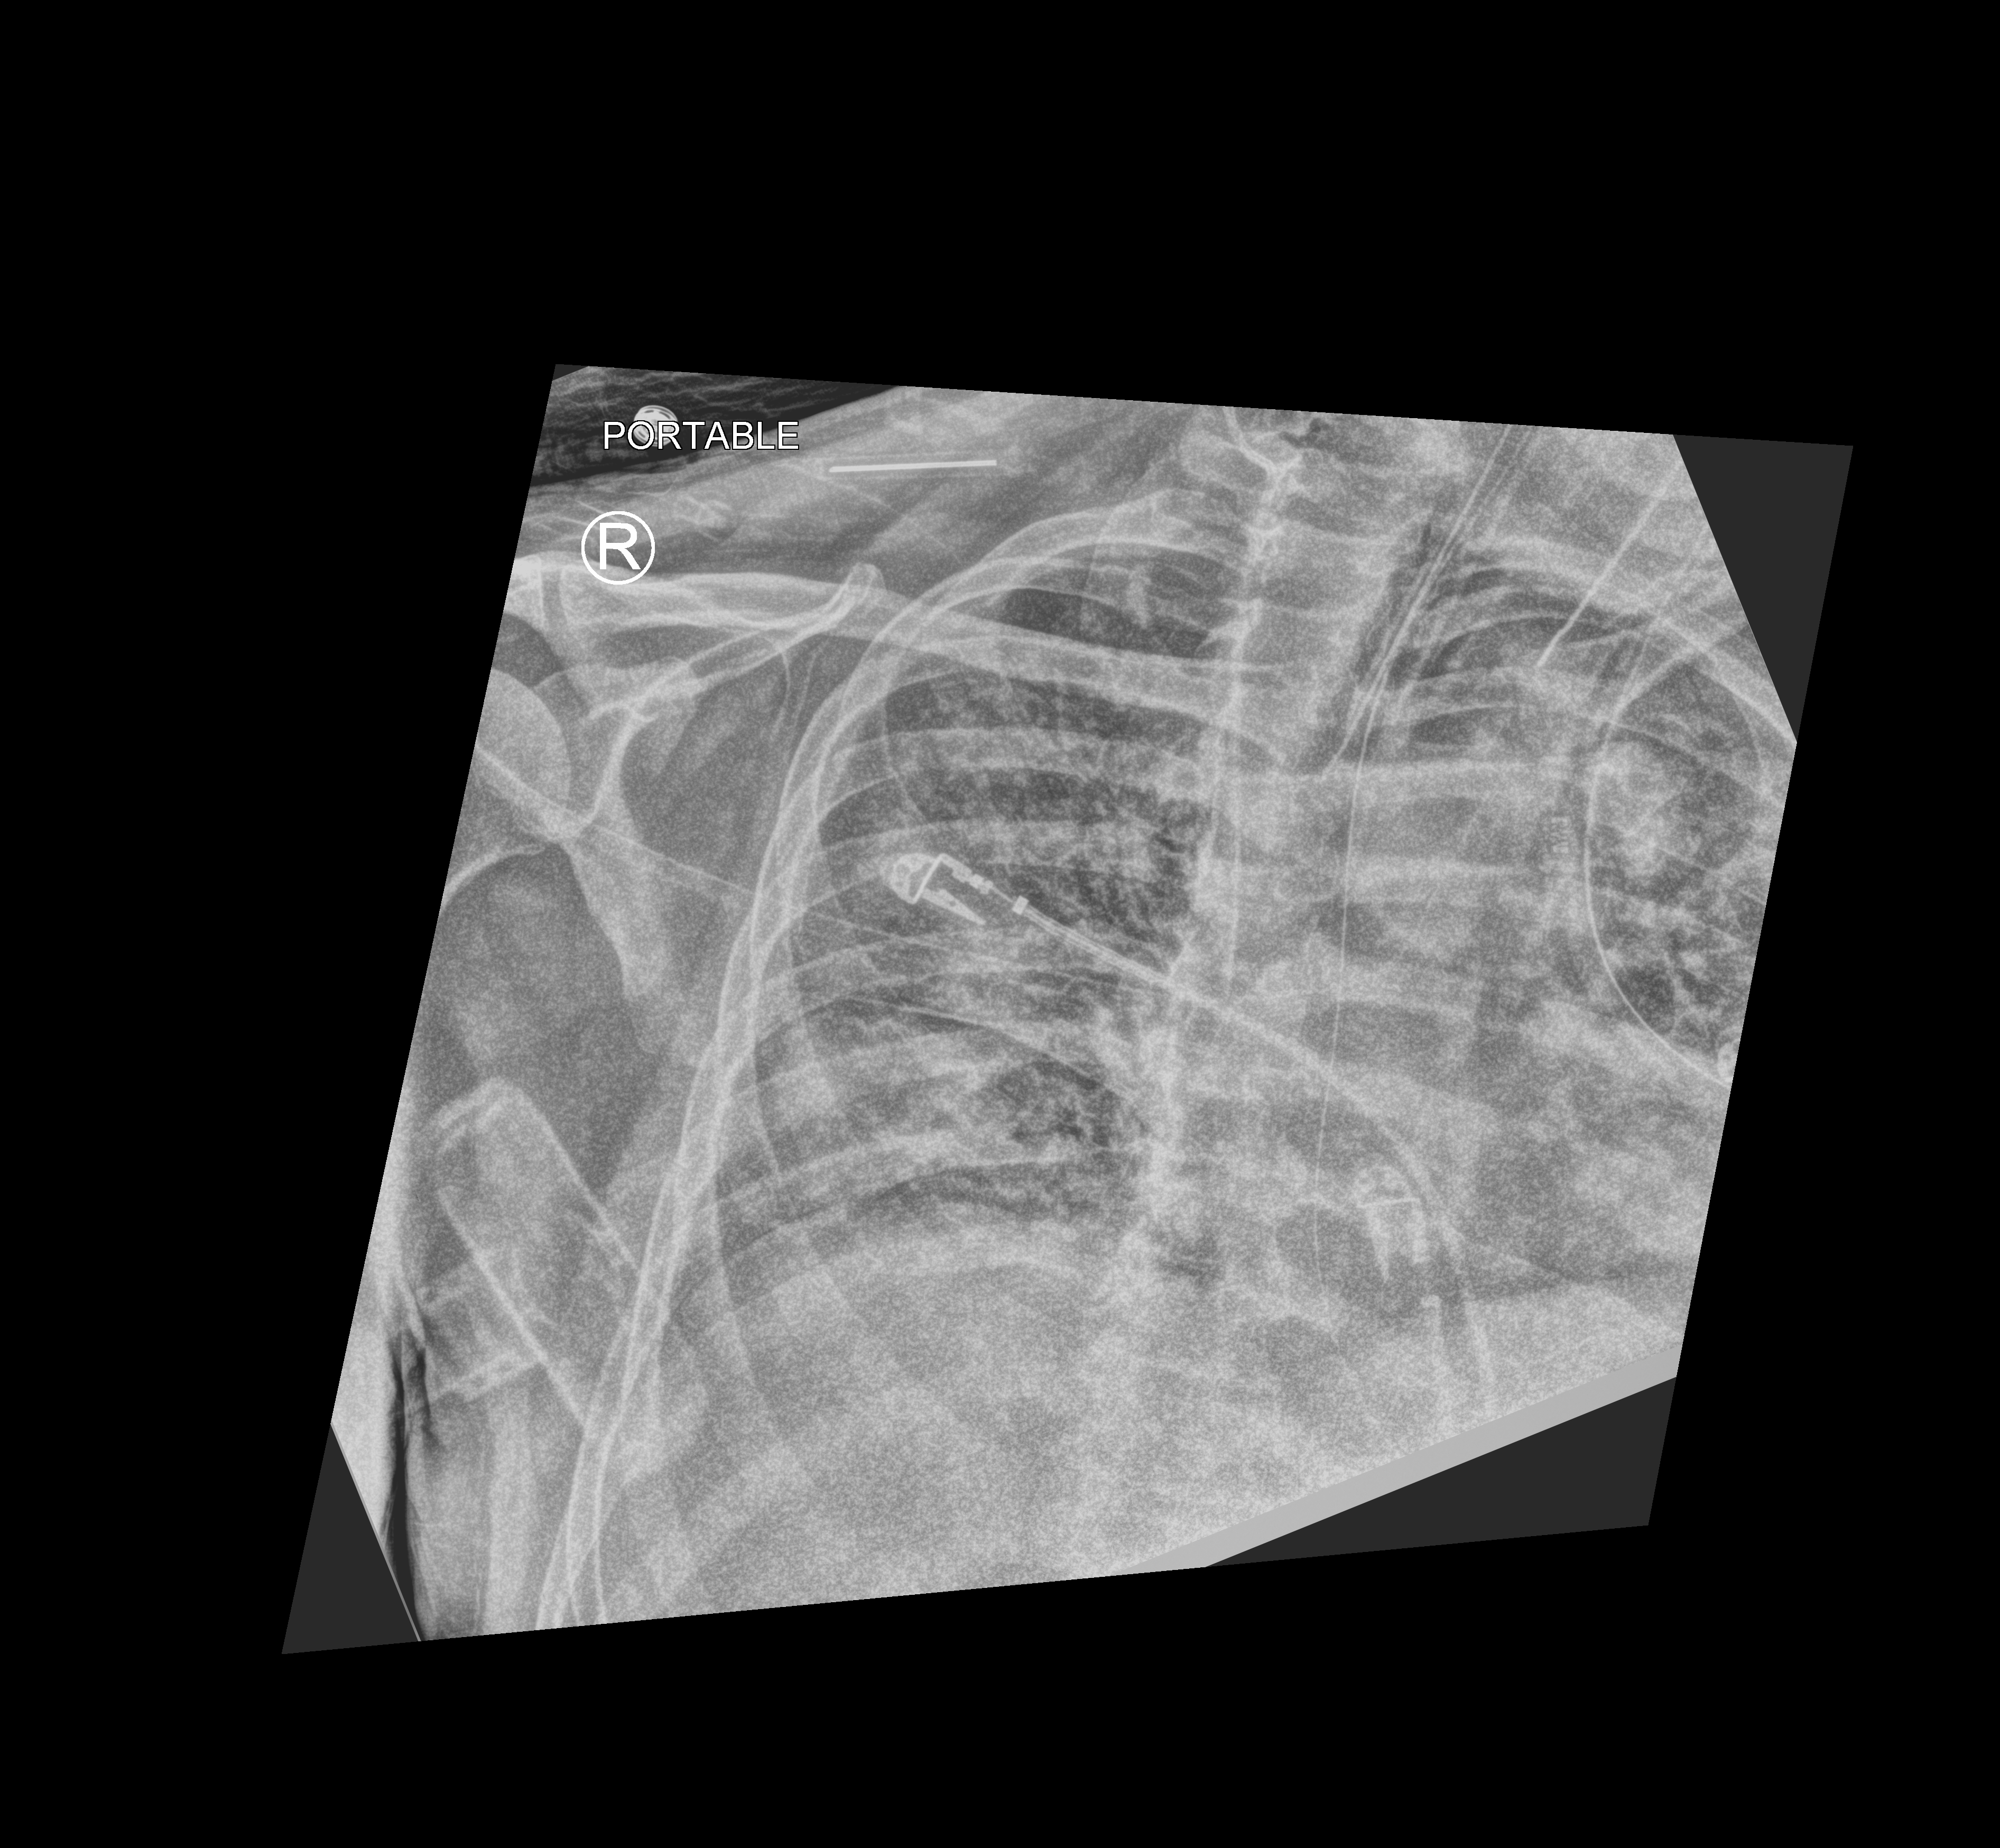
Bedside chest radiograph (computed radiography); anteroposterior (AP) projection. Male patient hospitalised with COVID-19, age 60–74 years.
Hospital-stay facts (about this admission, not read from this image; timing relative to this image not recorded):
- length of hospital stay: 33 days
- mechanically ventilated during this hospital stay: yes